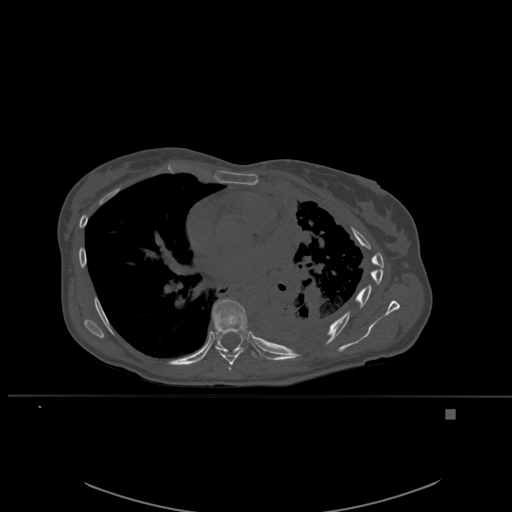
CT including the spine, one axial slice. Position 359 of 537 along the scan axis. Bone window (W 1800 / L 400 HU). 512 × 512 image matrix, field of view 440 × 440 mm. Patient: female, 45 years. Case-level facts recorded for this patient, not image findings: primary cancer: lung.
Outlined on this slice (semi-automatic segmentation, software-assisted and operator-edited):
- T6 vertebra: bounding box (x1, y1, x2, y2) in pixels: (228, 366, 232, 370)
- T7 vertebra: (216, 346, 248, 365)
- T8 vertebra: (212, 298, 255, 356)